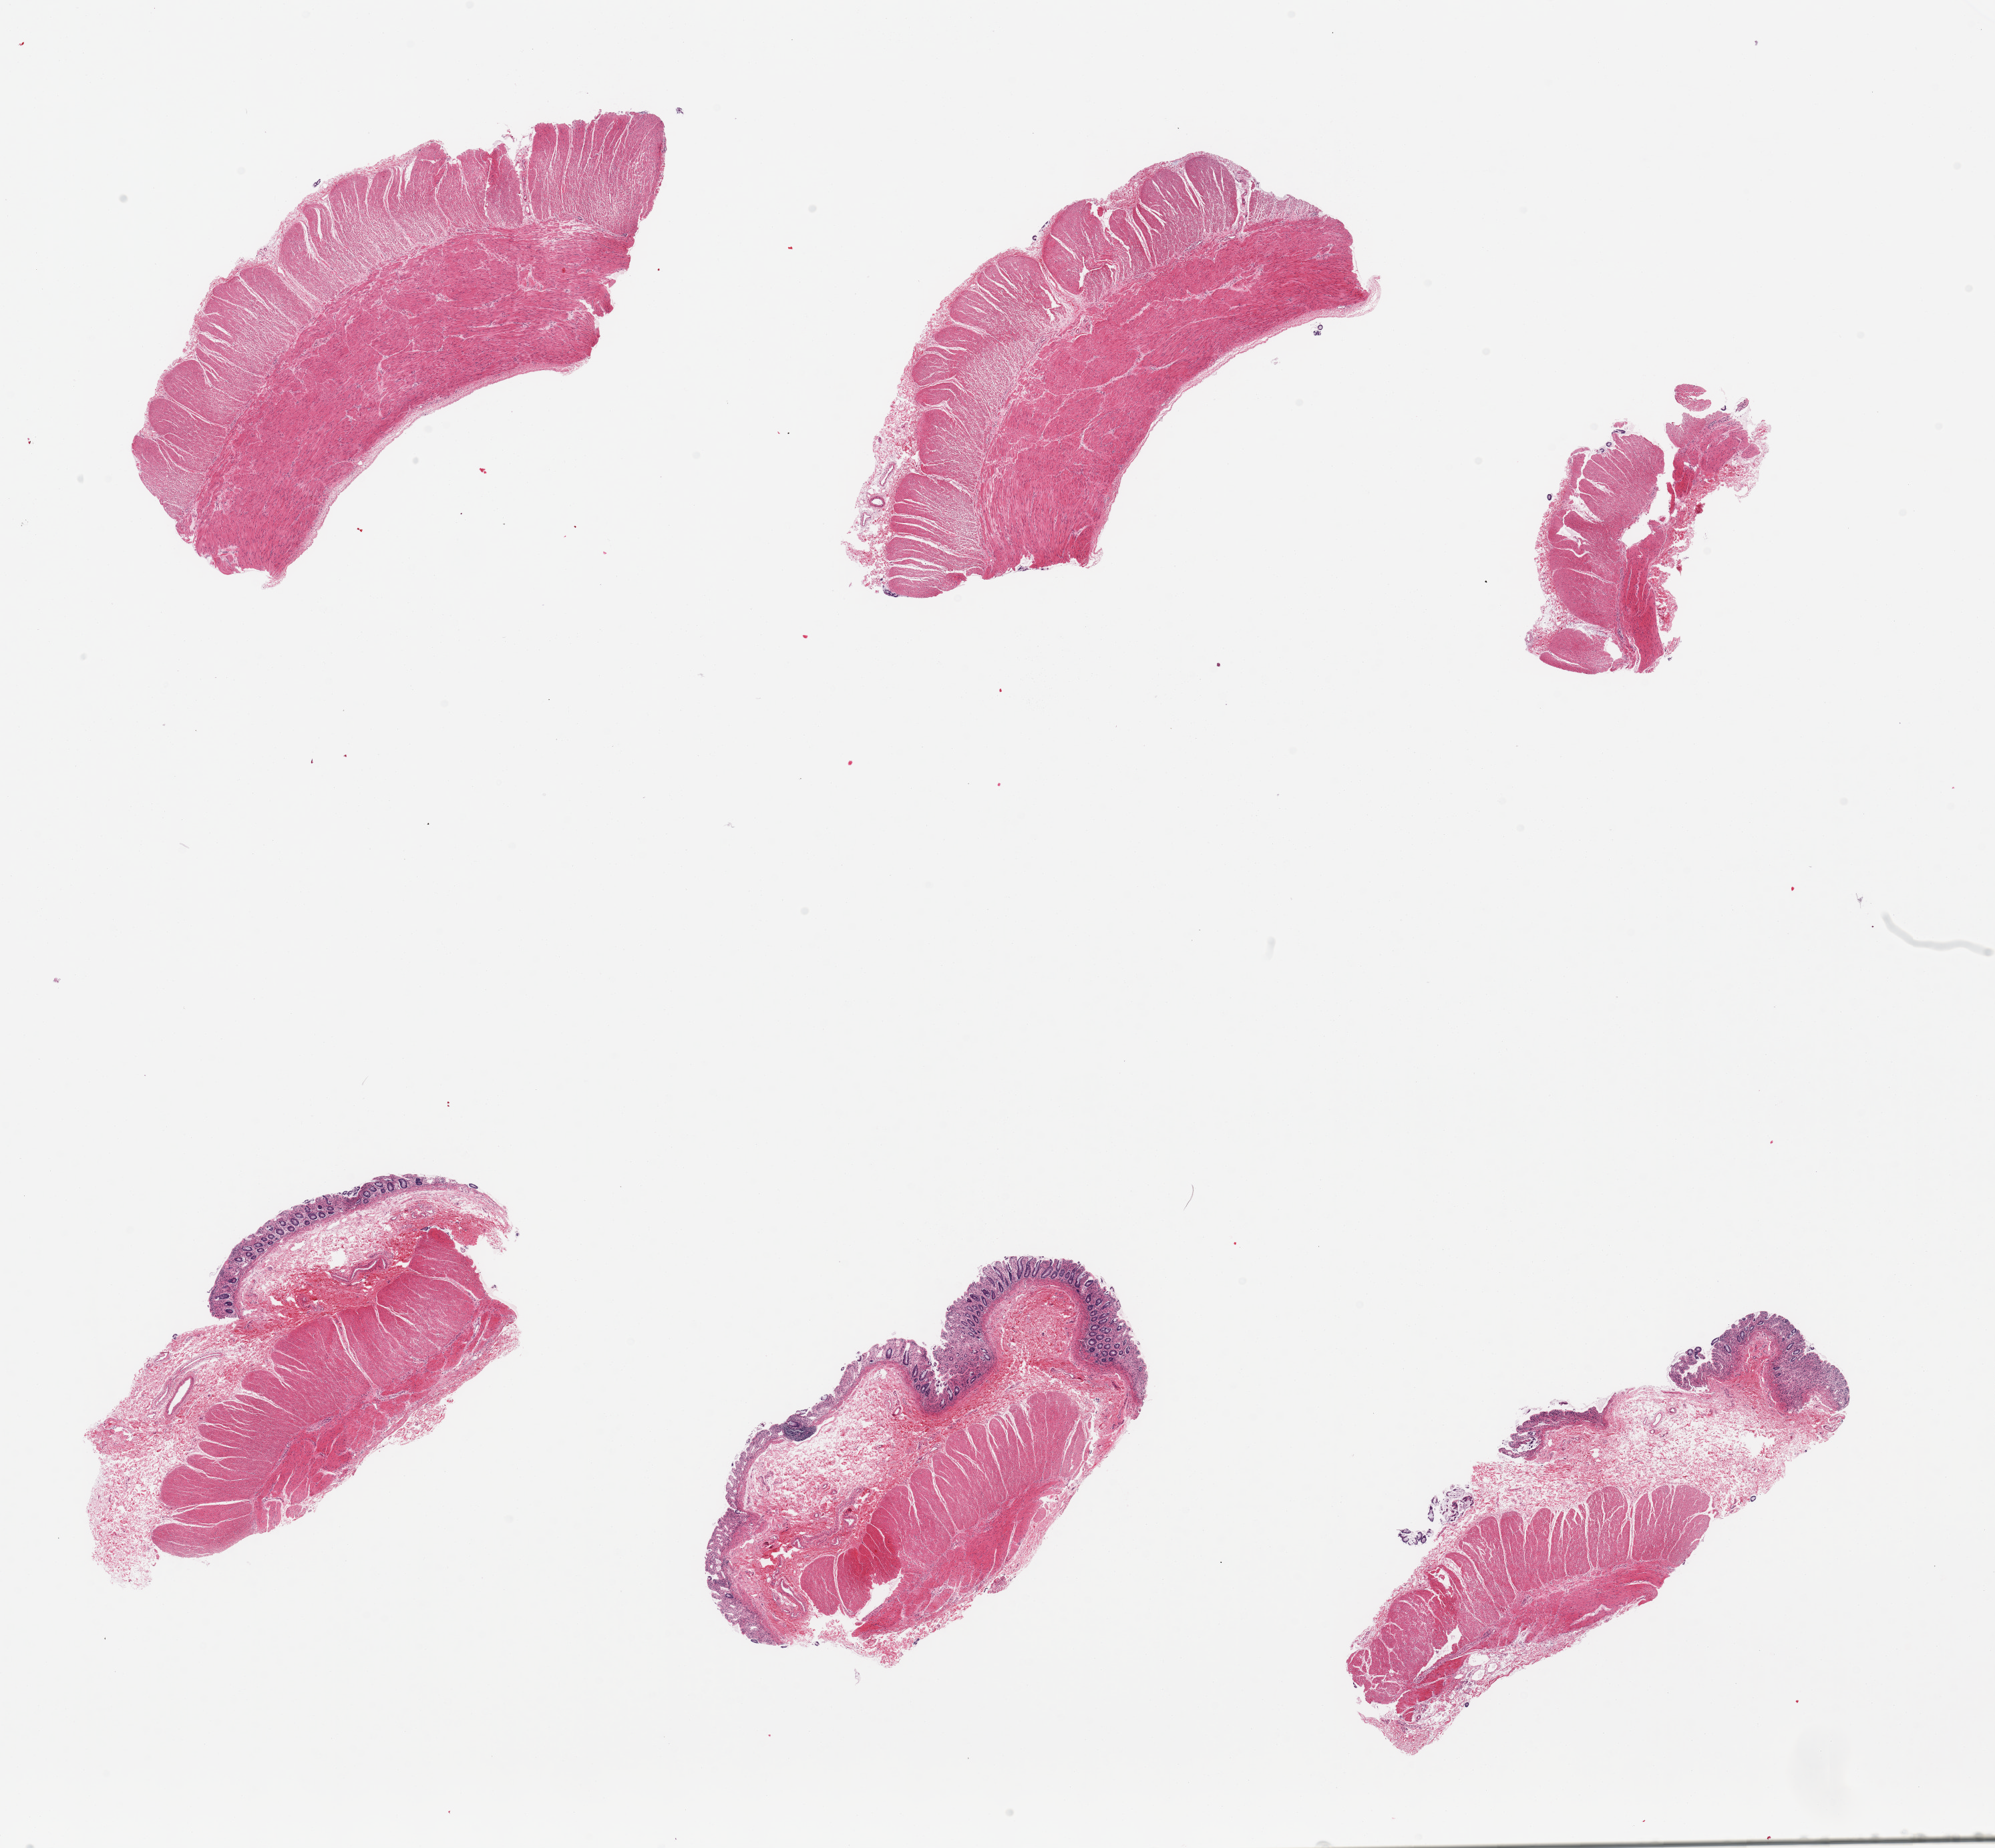
Whole-slide image, H&E stain, brightfield, low-resolution overview of the scanned area, about 23.6 x 21.9 mm (from a 20x scan).
Specimen: PAXgene-fixed paraffin-embedded (PFPE) section; target tissue: sigmoid colon; tissue donor sample.